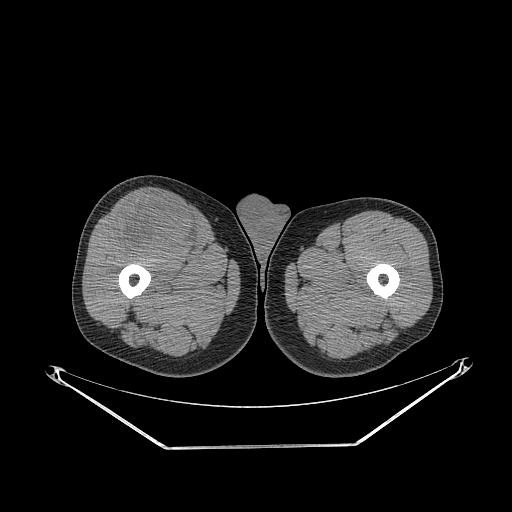
CT of an extremity soft-tissue mass (from a PET/CT study), one axial slice; position 277 of 311 along the scan axis; reconstruction kernel STANDARD; 140 kVp; soft-tissue window (W 400 / L 40 HU); 3.75 mm slice thickness; 512 × 512 image matrix. Male patient. From the clinical record (not read from this slice): histological type: pleiomorphic leiomyosarcoma; grade: intermediate; site of the primary tumour: right thigh.
Structures marked on this image (expert contour drawn on MRI and transferred to this co-registered scan by the dataset authors):
- gross tumour volume including surrounding oedema: box from (x=114, y=194) to (x=200, y=257) px
- gross tumour volume (mass): (x=114, y=194)–(x=200, y=257)